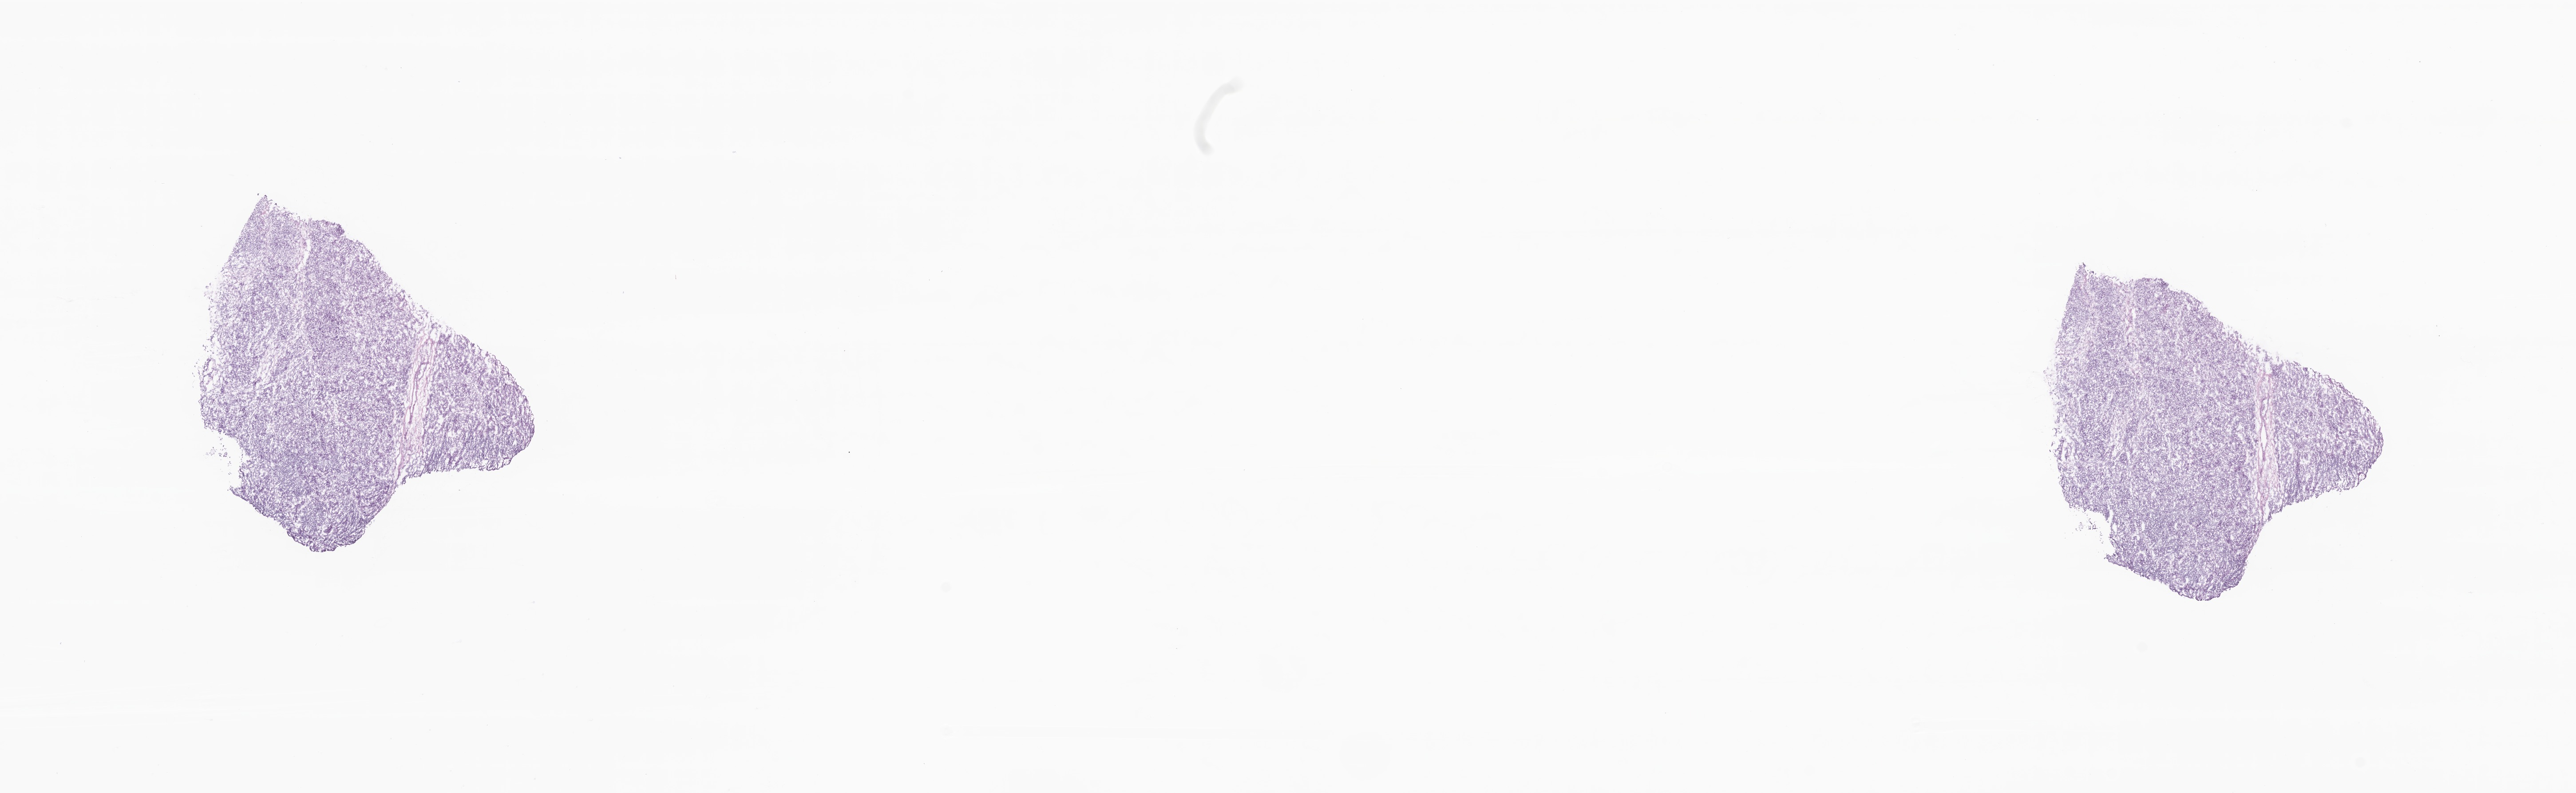
Hematoxylin and eosin (H&E) whole-slide image — a low-resolution overview of the entire scanned area, about 24.5 x 7.5 mm. Cryosection. Metastatic tumor tissue. Female patient; age at initial diagnosis 54 years. Composition of this section per pathologist review: tumor cells 90%, tumor nuclei 90%, stromal cells 10%, necrosis 0%, normal cells 0%. Inflammatory infiltration, as recorded: lymphocyte infiltration 0%, monocyte infiltration 0%, neutrophil infiltration 0%.
Patient diagnosis (primary): Infiltrating duct carcinoma, NOS.